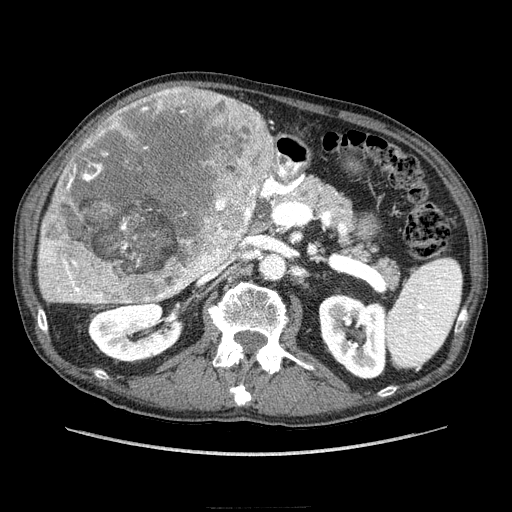
Contrast-enhanced abdominal CT (liver protocol), one axial slice. Slice 123 of 218 in the series (ordered by position). Reconstruction kernel STANDARD. 100 kVp. Soft-tissue window (W 400 / L 40 HU). 512 × 512 image matrix, field of view 380 × 380 mm. From the clinical record (not read from this slice): diagnosis: hepatocellular carcinoma (patient treated with transarterial chemoembolisation; whether this scan precedes or follows treatment is not stated here); TNM stage (as recorded): Stage-IIIA.
Outlined on this slice (semi-automatically segmented with operator editing):
- liver parenchyma outside the tumour (the mass and vessels are separate outlines, so this box may not span the whole liver): box from (x=38, y=90) to (x=276, y=304) px
- mass: (x=43, y=81)–(x=276, y=305)
- liver vessels: (x=40, y=254)–(x=103, y=302)